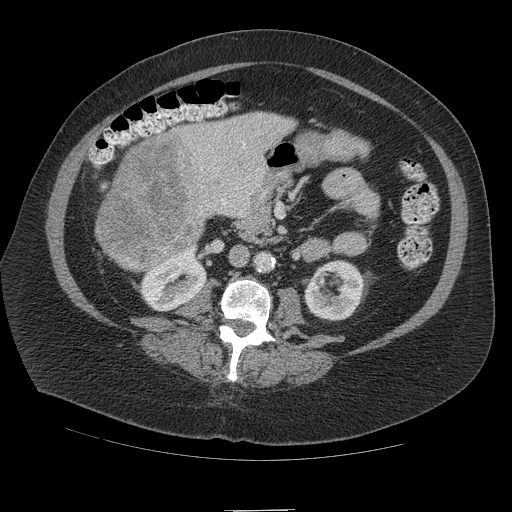
Contrast-enhanced abdominal CT (liver protocol), one axial slice. Slice 35 of 109 in the series (ordered by position). 140 kVp. Soft-tissue window (W 400 / L 40 HU). 512 × 512 image matrix. From the clinical record (not read from this slice): diagnosis: hepatocellular carcinoma (patient treated with transarterial chemoembolisation; whether this scan precedes or follows treatment is not stated here); TNM stage (as recorded): Stage-IVB; Child-Pugh class: A; tumour differentiation: poorly differentiated.
Annotated regions visible in this slice (semi-automatic segmentation, software-assisted and operator-edited):
- liver parenchyma outside the tumour (the mass and vessels are separate outlines, so this box may not span the whole liver): bounding box (x1, y1, x2, y2) in pixels: (96, 112, 294, 248)
- mass: (96, 133, 205, 270)
- liver vessels: (199, 143, 249, 205)